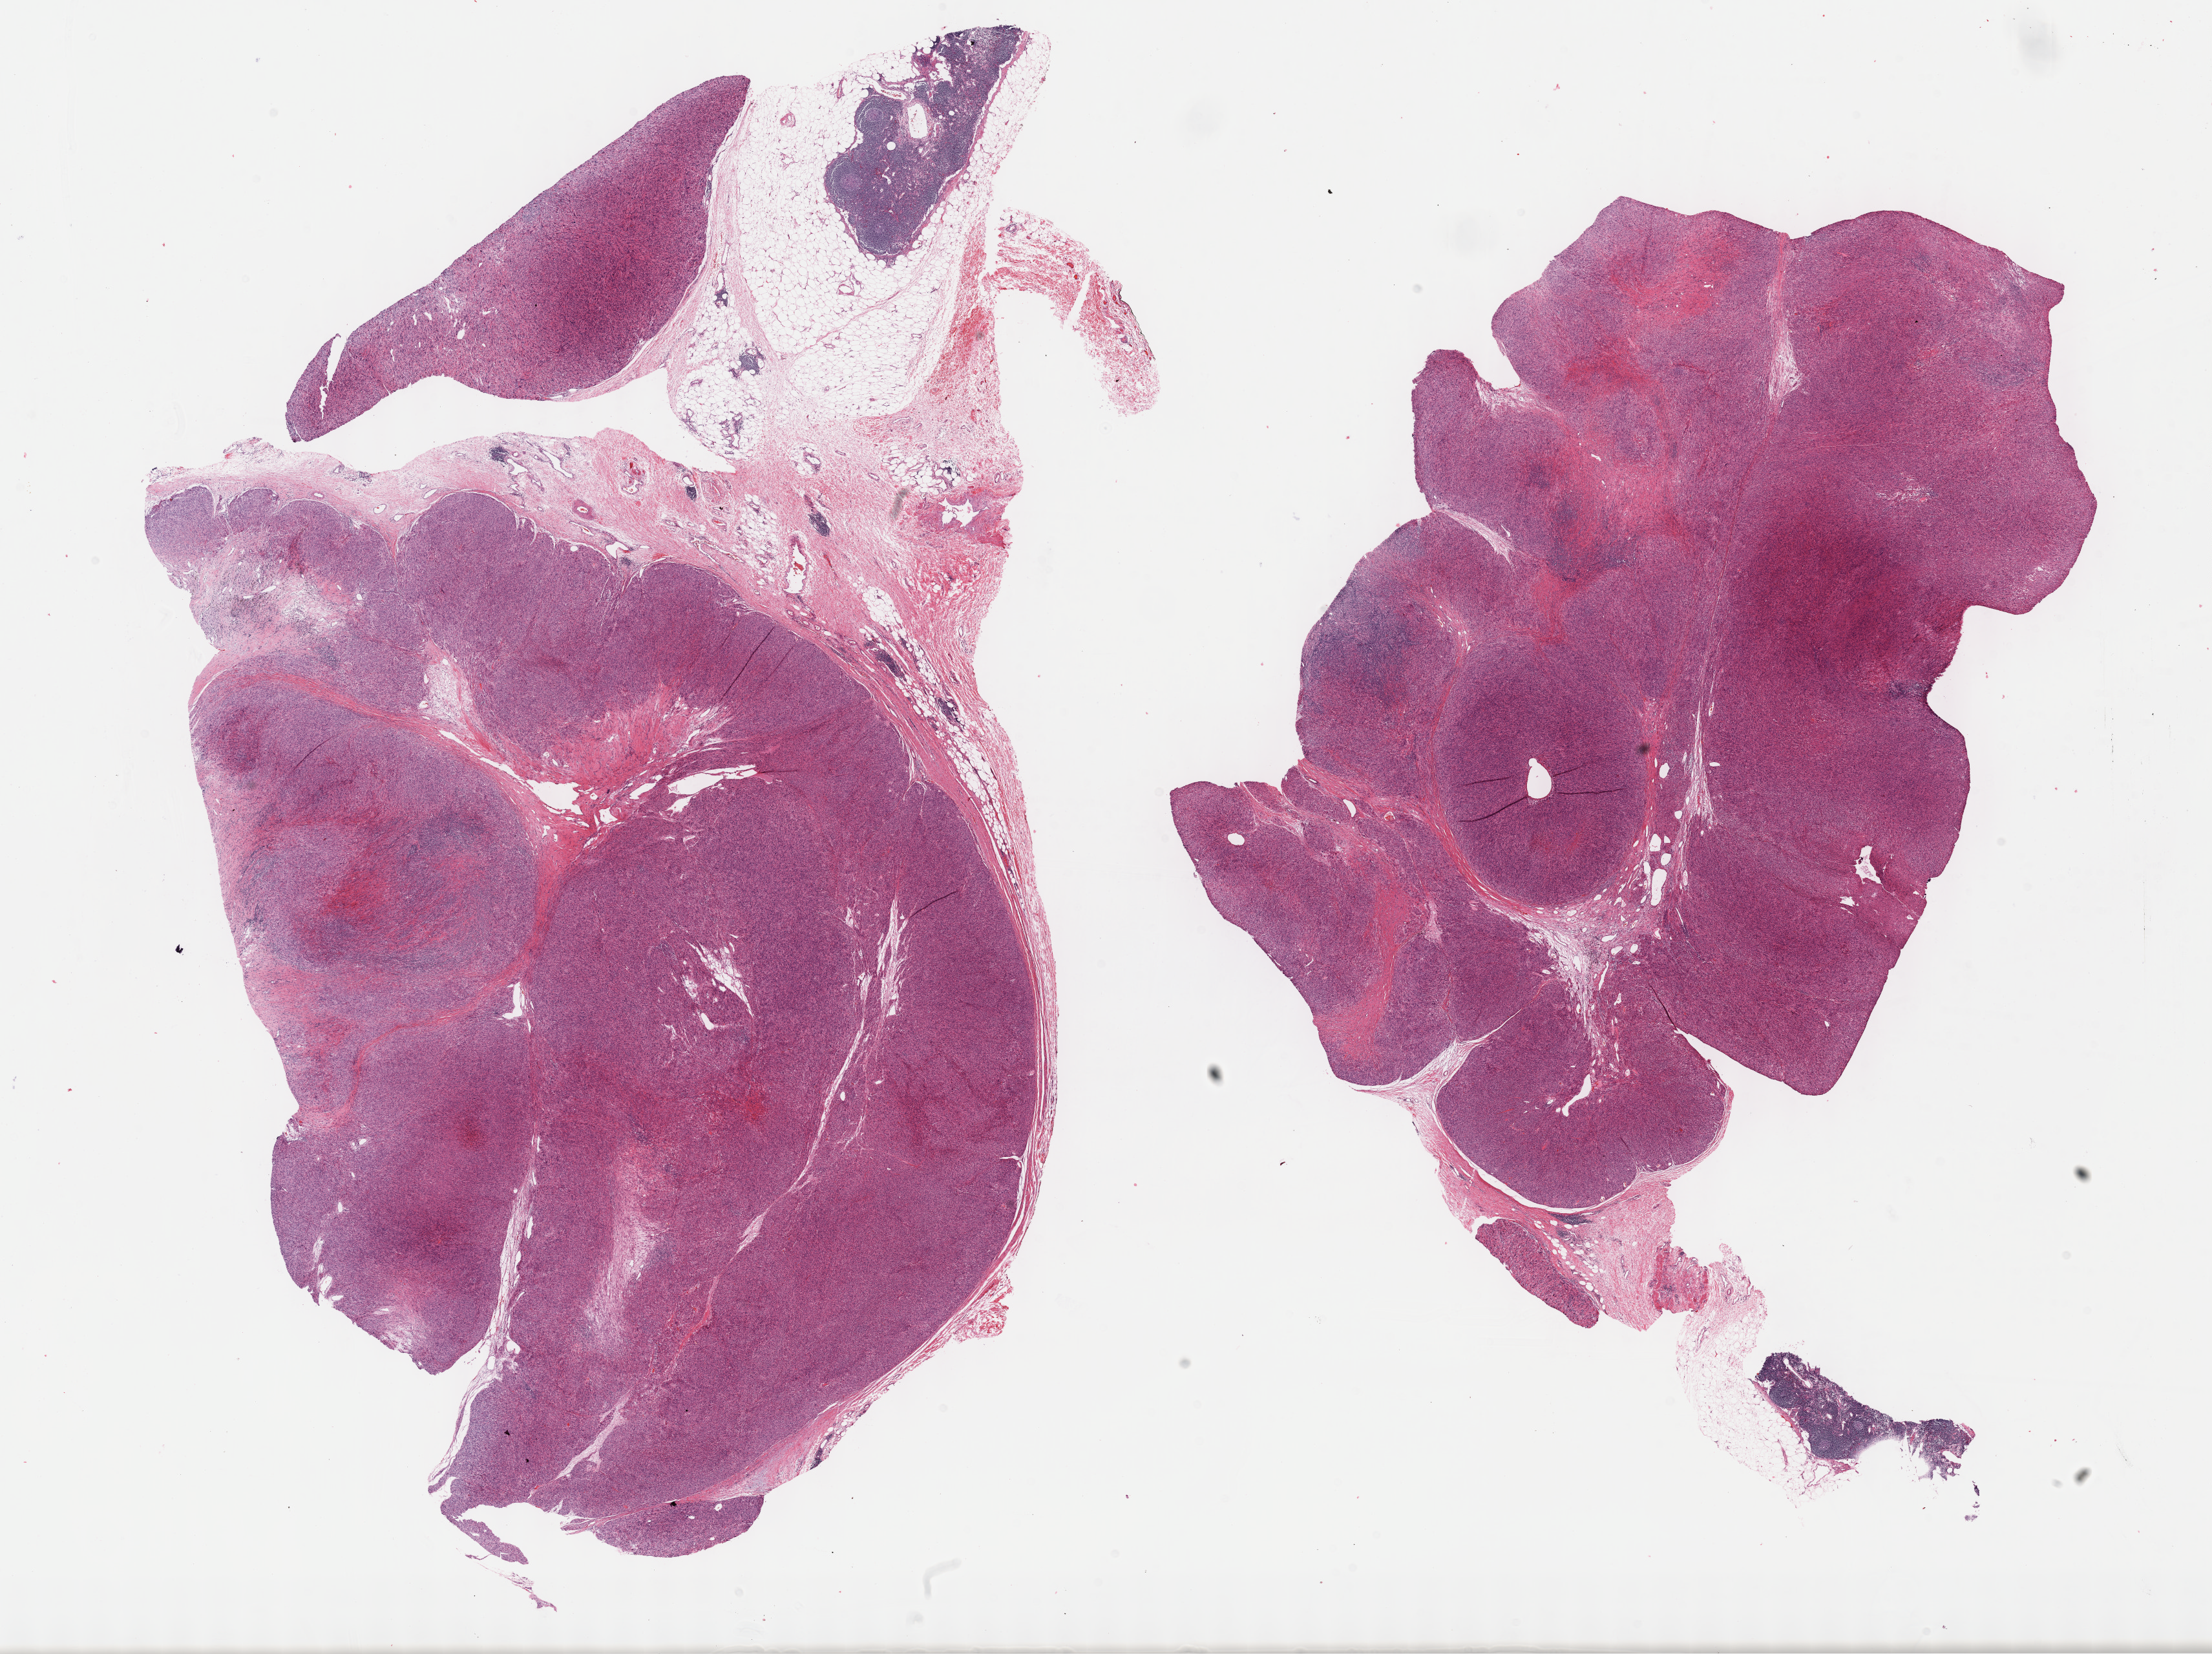
Digitized H&E-stained tissue section (whole slide), shown as a low-resolution overview of the whole scanned area (about 27.7 x 20.7 mm, from a 40x scan), formalin-fixed paraffin-embedded (FFPE) diagnostic section, primary tumour sample from the retroperitoneum and peritoneum. Patient: male, age at initial diagnosis 70 years.
Diagnosis: Leiomyosarcoma, NOS (retroperitoneum).